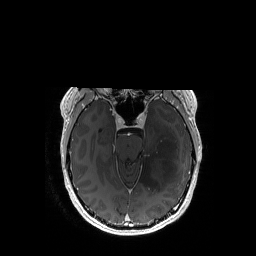
Brain MRI from a brain-tumour surgery series, one axial slice; position 111 of 192 along the scan axis; T1-weighted post-contrast; 1 mm slice thickness; 256 × 256 image matrix. Case-level facts recorded for this patient, not image findings: histopathology: Astrocytoma; WHO grade: 3; IDH mutation: yes; tumour location: Left Temporal.
Outlined on this slice (expert manual segmentation):
- tumour: box from (x=139, y=126) to (x=178, y=191) px